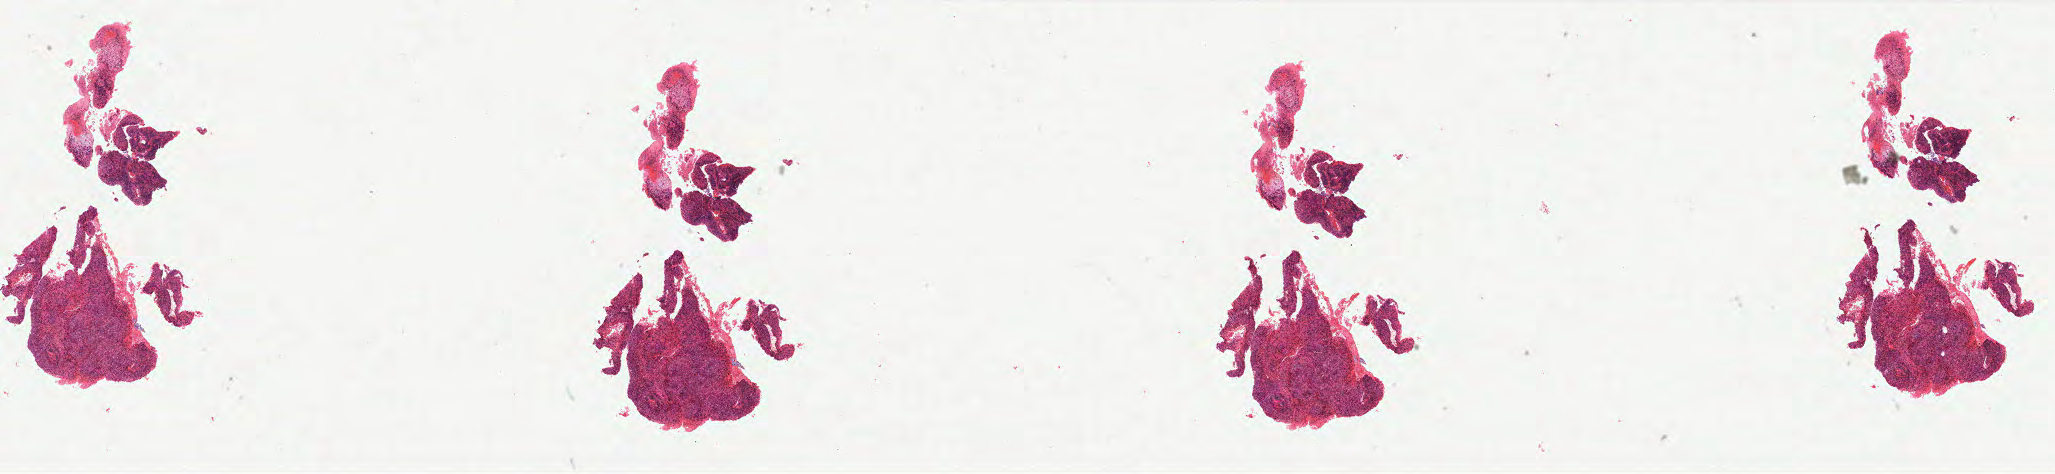
Digitized H&E-stained tissue section (whole slide) — a low-resolution overview of the entire scanned area, about 32.9 x 7.6 mm. FFPE section. Cervix, primary tumour sample. Female, age 72 years at initial diagnosis.
Pathologic diagnosis: Squamous cell carcinoma, keratinizing, NOS (cervix uteri).